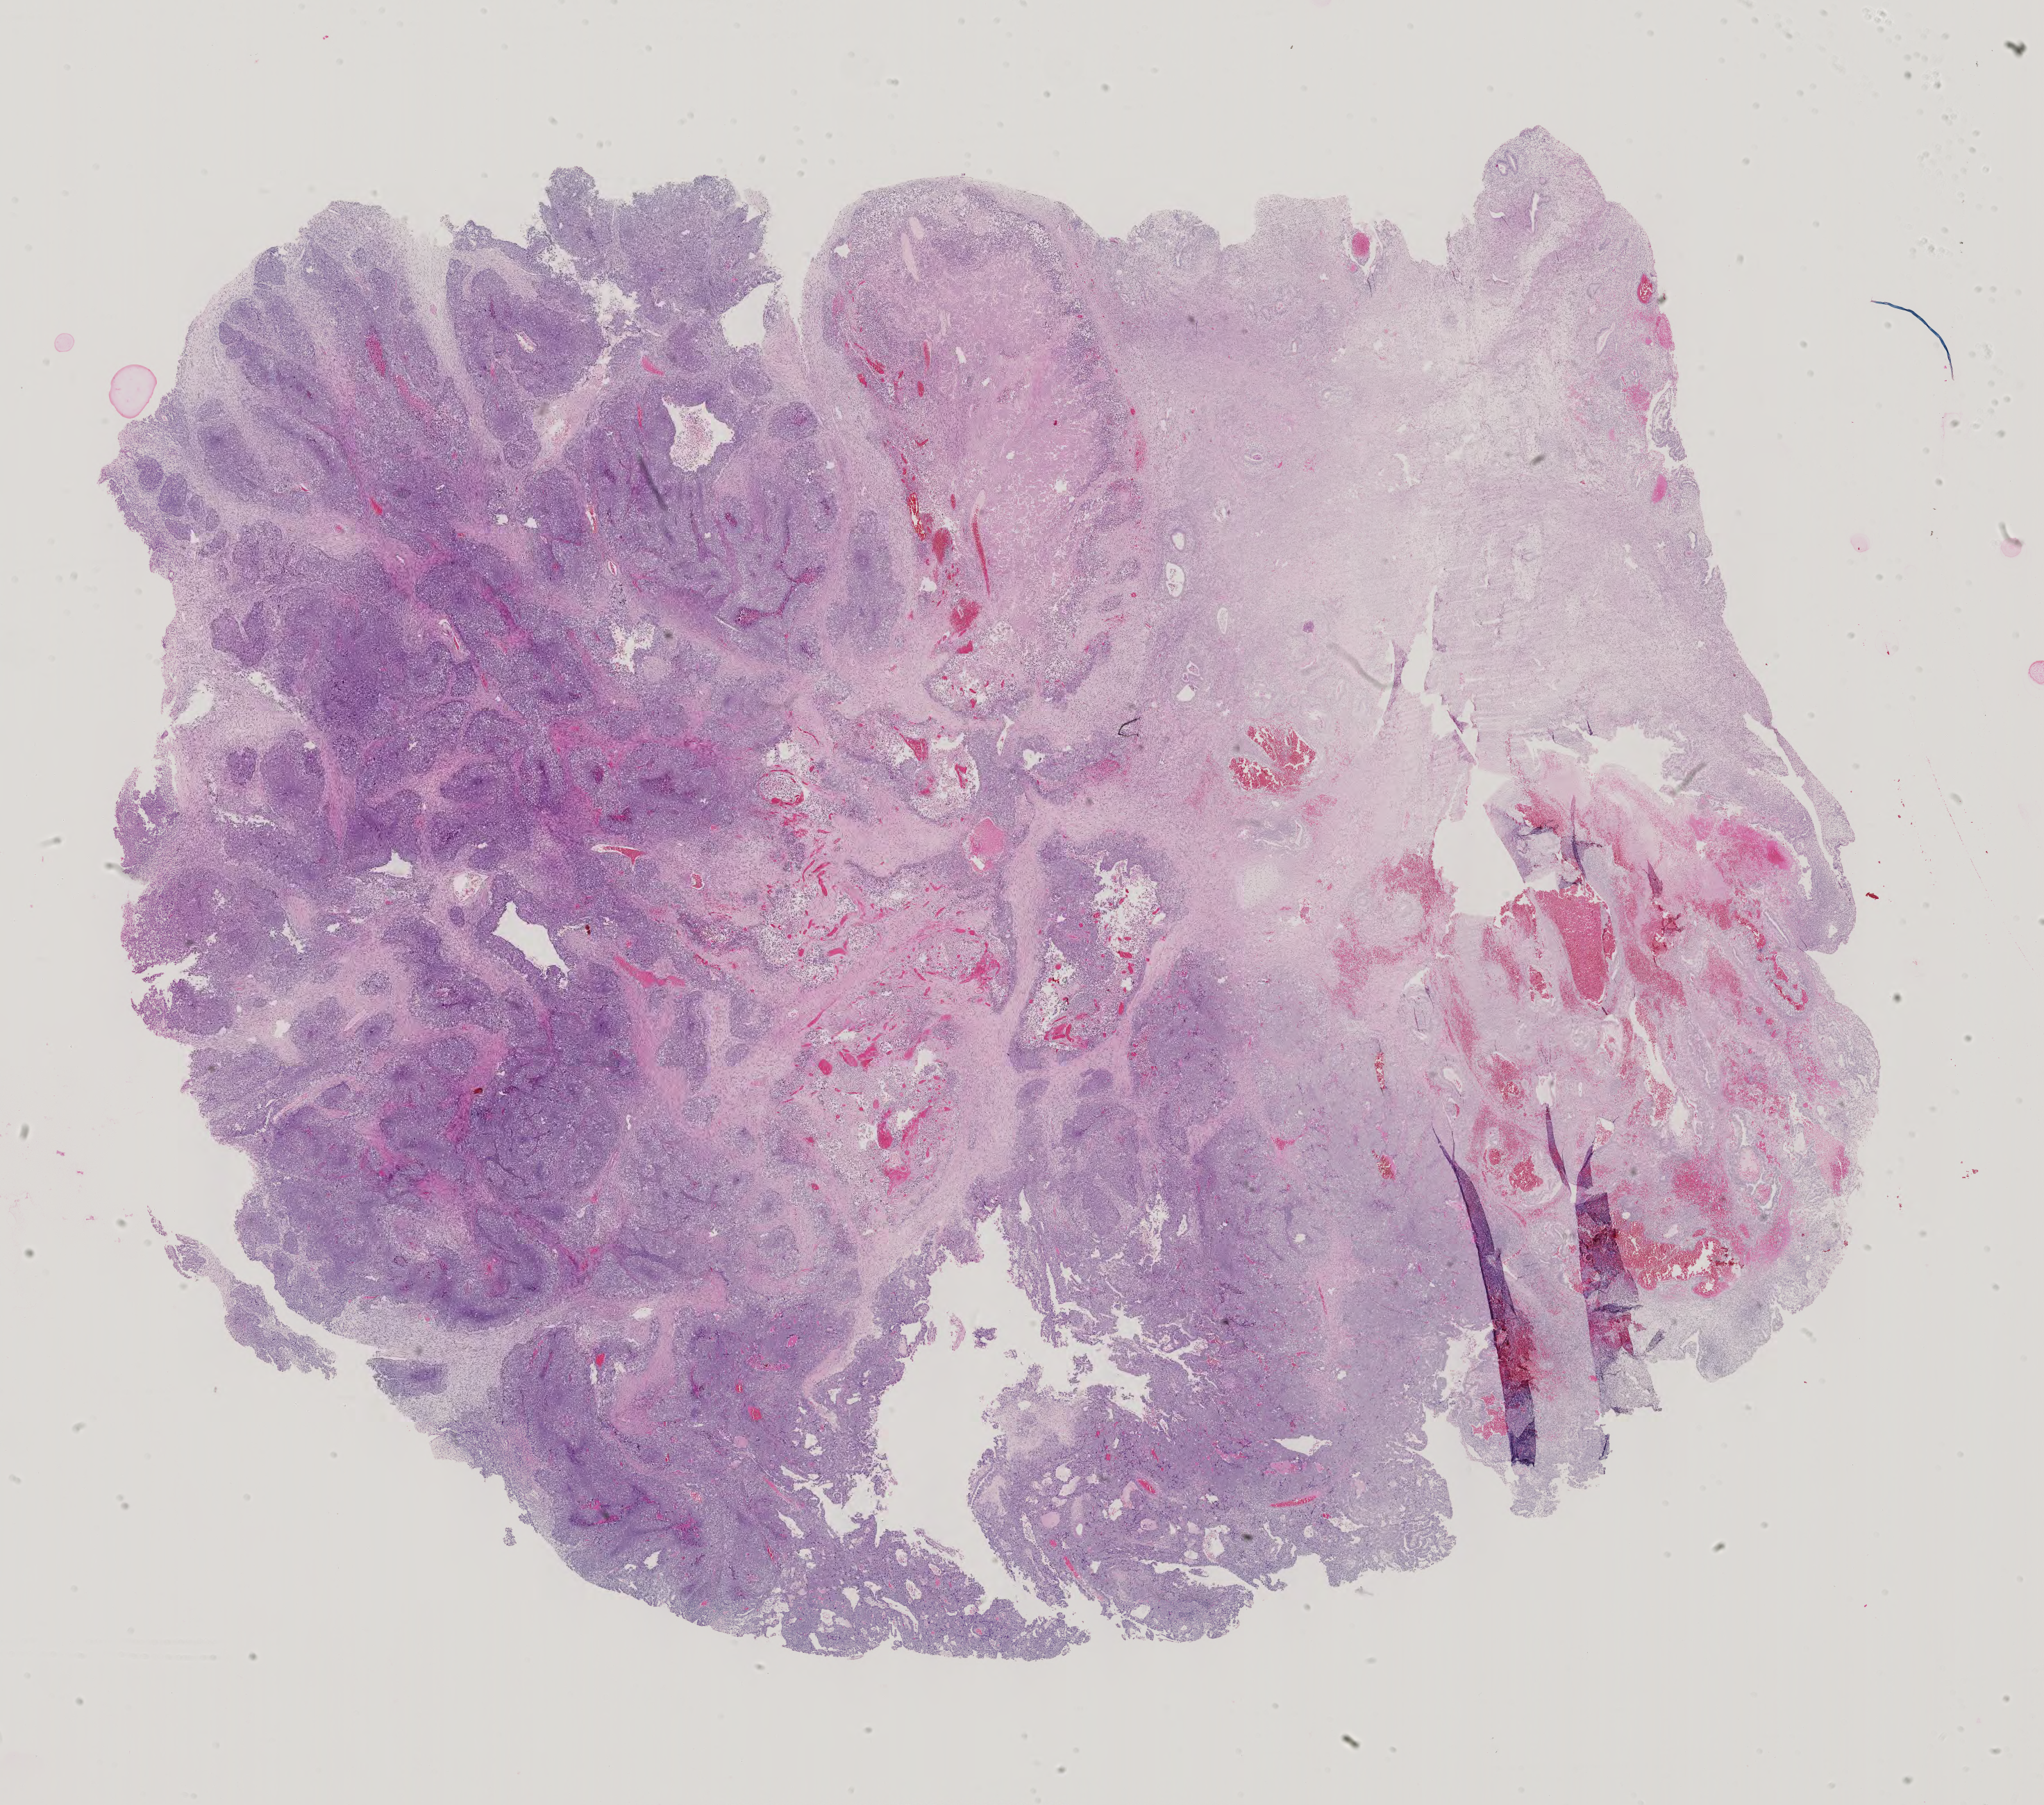
H&E-stained whole-slide image, whole scanned area (about 21.5 x 18.9 mm, slide scanned at 40x) shown as a low-resolution overview. Patient sex: male.
Specimen: formalin-fixed paraffin-embedded (FFPE) diagnostic section; testis, primary tumour sample.